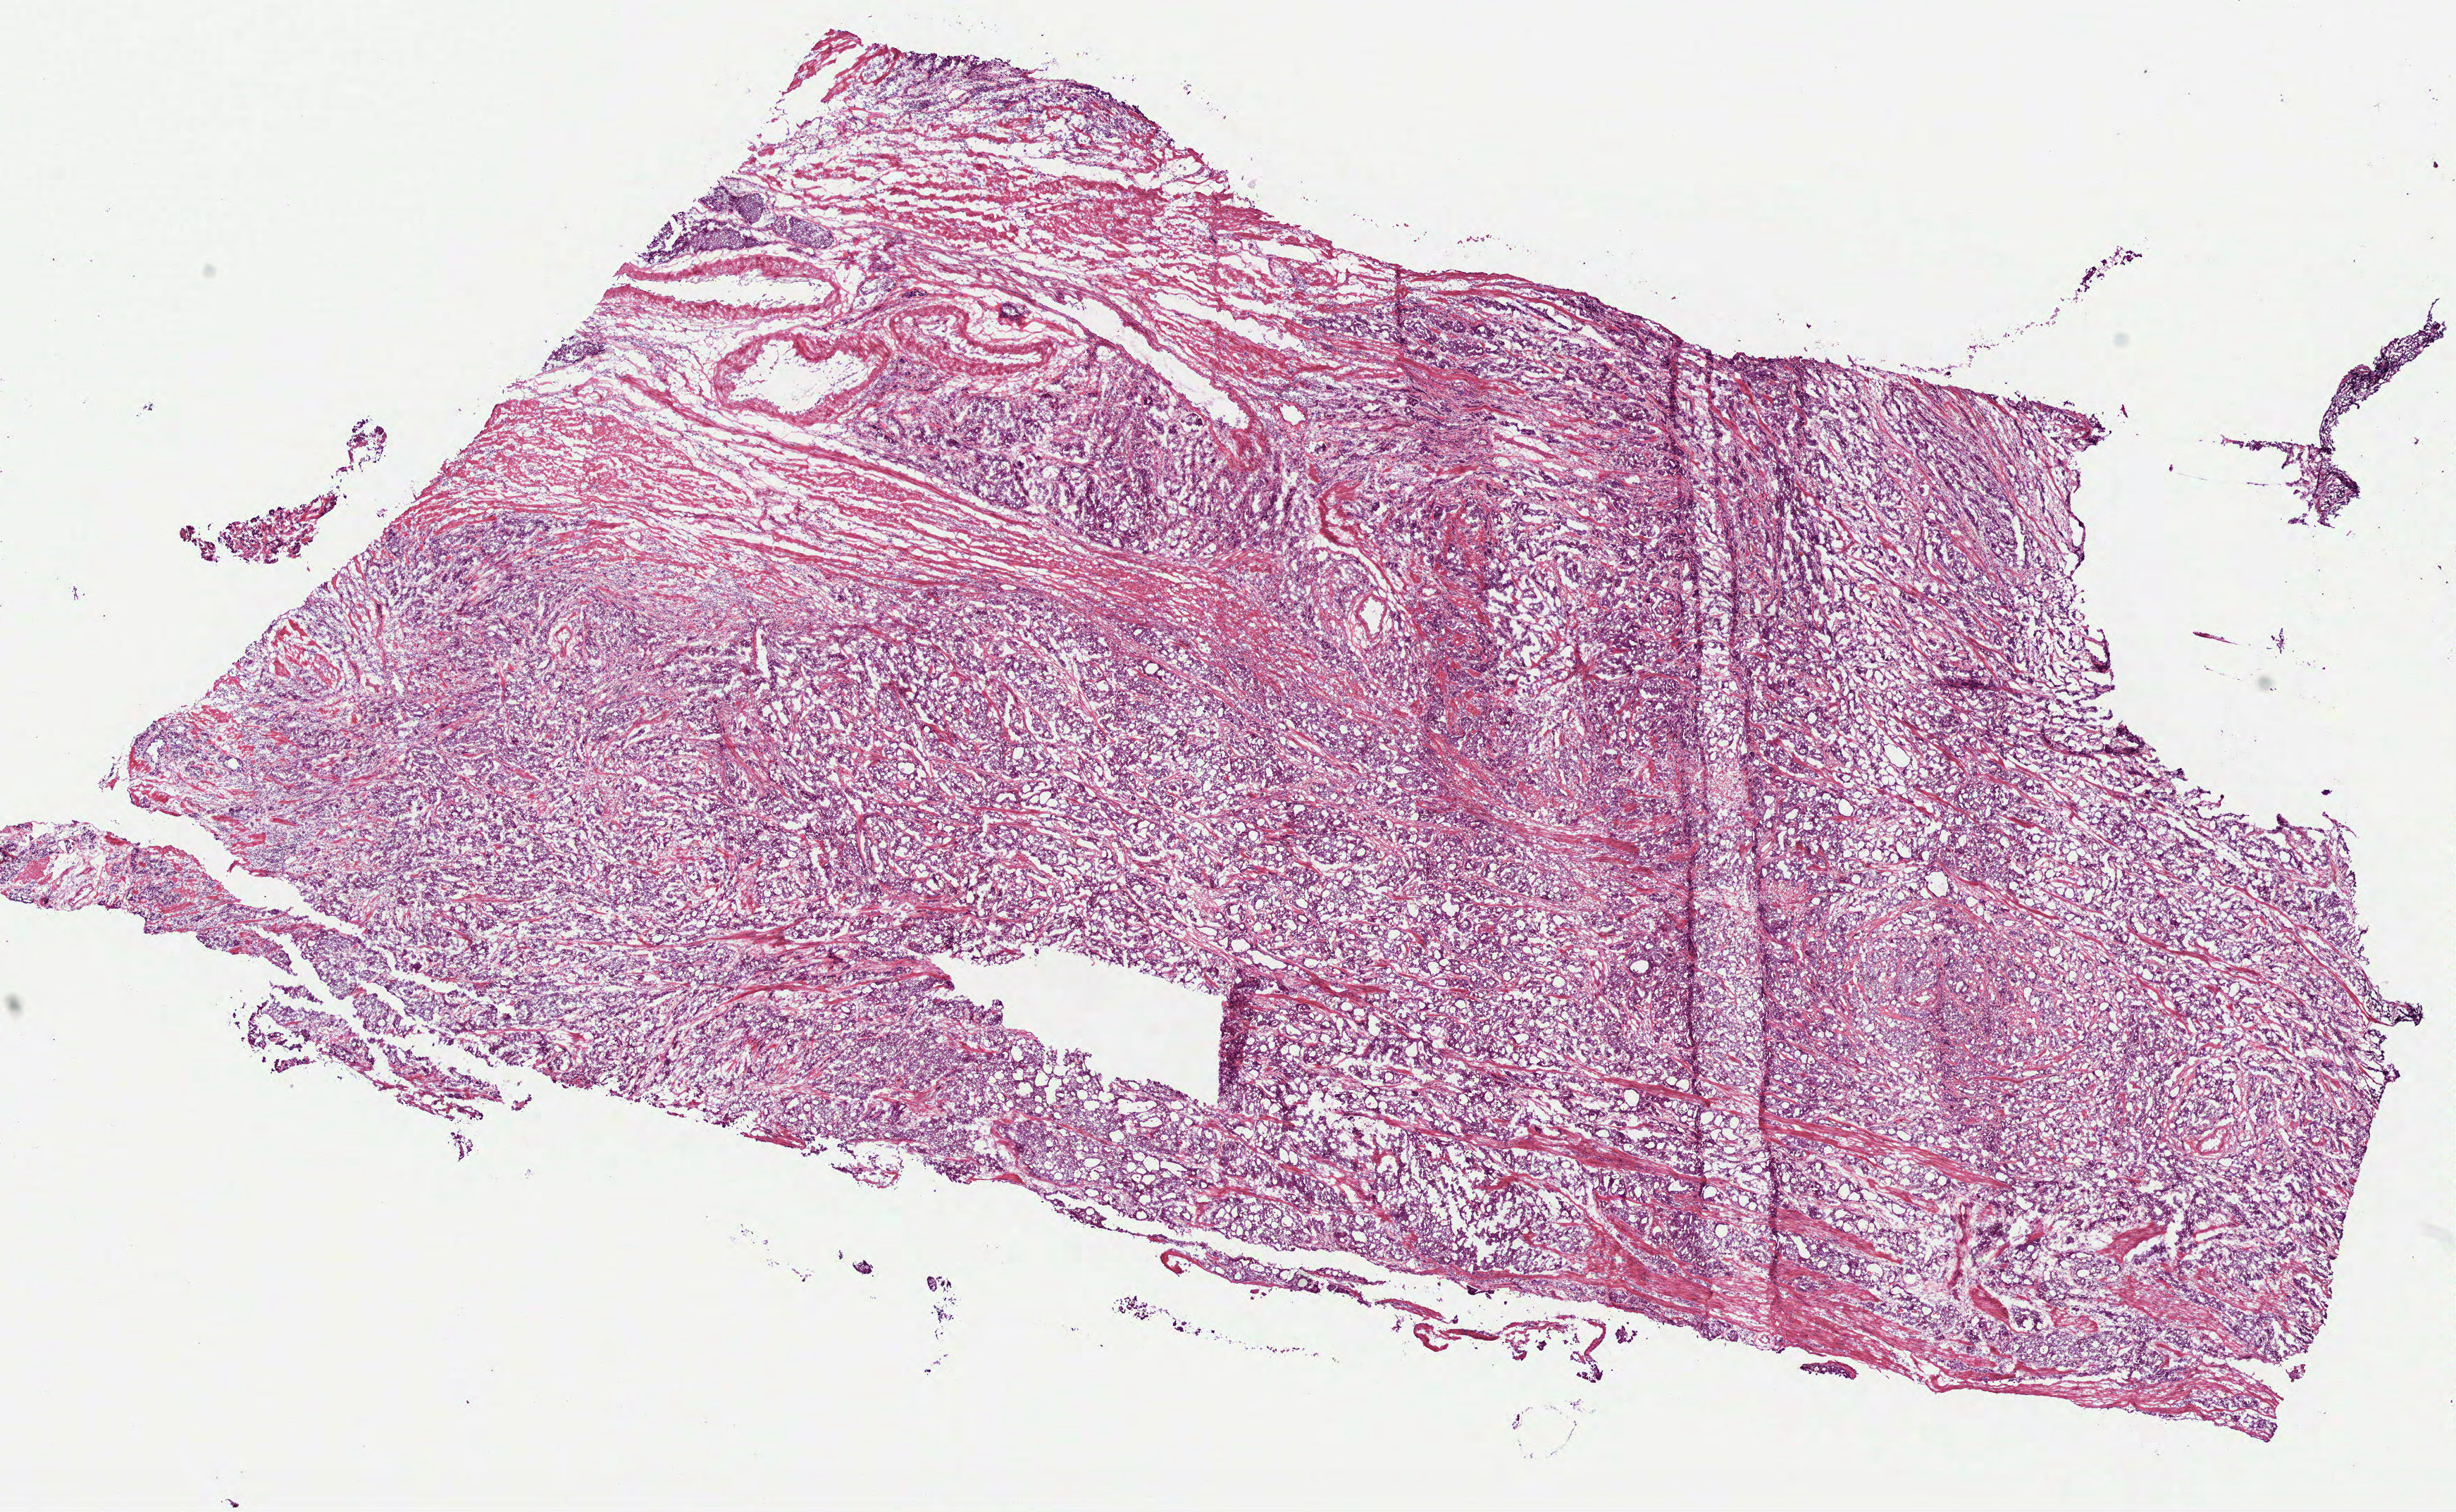
Whole-slide histology image, H&E-stained, a low-resolution overview of the entire scanned area, about 14.1 x 8.7 mm (slide scanned at 40x); frozen section from the bottom of the tissue portion; stomach, primary tumour sample. Female patient; age at initial diagnosis 72 years. Histologic grade: G2 (moderately differentiated). Composition of this section per pathologist review: tumour cells 90%, tumour nuclei 80%, normal cells 0%, stromal cells 10%, necrosis 0%.
AJCC pathologic stage: II (6th edition). Diagnosis: Adenocarcinoma, intestinal type (gastric antrum).